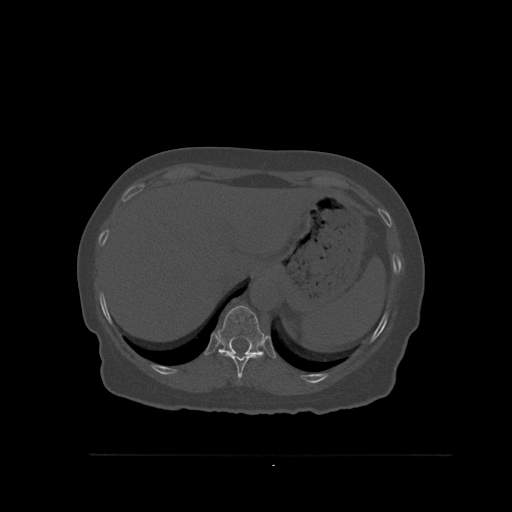
CT including the spine, one axial slice; slice 310 of 527 in the series (ordered by position); bone window (W 1800 / L 400 HU); 1.5 mm slice thickness; 512 × 512 image matrix, field of view 470 × 470 mm. Patient: female, 73 years. Case-level facts recorded for this patient, not image findings: primary cancer: breast.
Outlined on this slice (semi-automatically segmented with operator editing):
- T10 vertebra: bounding box (x1, y1, x2, y2) in pixels: (218, 349, 264, 384)
- T11 vertebra: (217, 305, 265, 356)